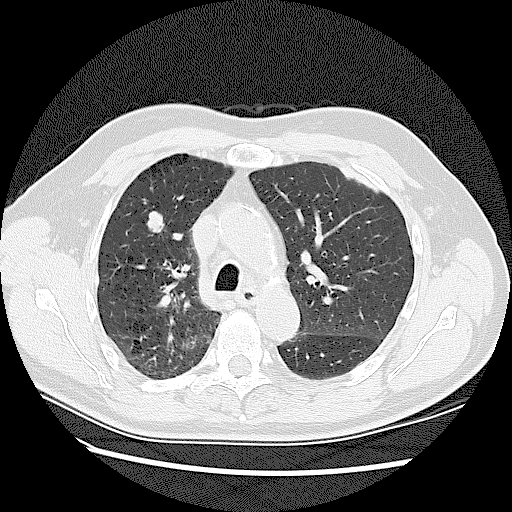
Low-dose screening chest CT, one axial slice. Reconstruction kernel LUNG. Lung window (W 1500 / L -600 HU). 2.5 mm slice thickness. 512 × 512 image matrix, field of view 360 × 360 mm.
Annotated regions visible in this slice (manually delineated by an expert):
- lesion 1 (tumor, upper lobe of right lung): box from (x=147, y=211) to (x=164, y=233) px